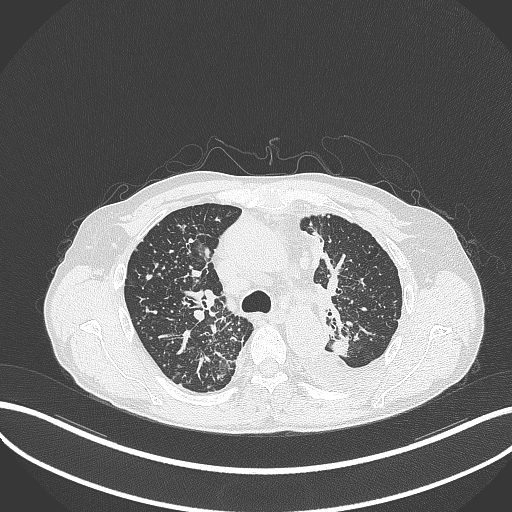
Chest CT, one axial slice; position 249 of 325 along the scan axis; reconstruction kernel B70f; 120 kVp; lung window (W 1500 / L -600 HU); 1 mm slice thickness; 512 × 512 image matrix, field of view 400 × 400 mm. Patient: male, 58 years. From the clinical record (not read from this slice): clinical TNM (as recorded): T1c N3 M1.
Annotated regions visible in this slice (rectangle marked by the reading radiologist):
- lung tumour (recorded histology: adenocarcinoma): bounding box <331,333,353,358> (left, top, right, bottom; pixels)